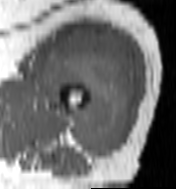
MRI of an extremity soft-tissue mass, one axial slice; position 72 of 100 along the scan axis; MR volume resampled by the dataset authors to the PET/CT grid (not the native acquisition matrix); 3.27 mm slice thickness; 176 × 189 image matrix. Female patient. From the clinical record (not read from this slice): histological type: undifferentiated – high grade; grade: high; site of the primary tumour: left thigh.
Annotated regions visible in this slice (expert contour drawn on MRI and transferred to this co-registered scan by the dataset authors):
- gross tumour volume including surrounding oedema: box from (x=44, y=34) to (x=136, y=158) px
- gross tumour volume (mass): (x=44, y=34)–(x=136, y=158)